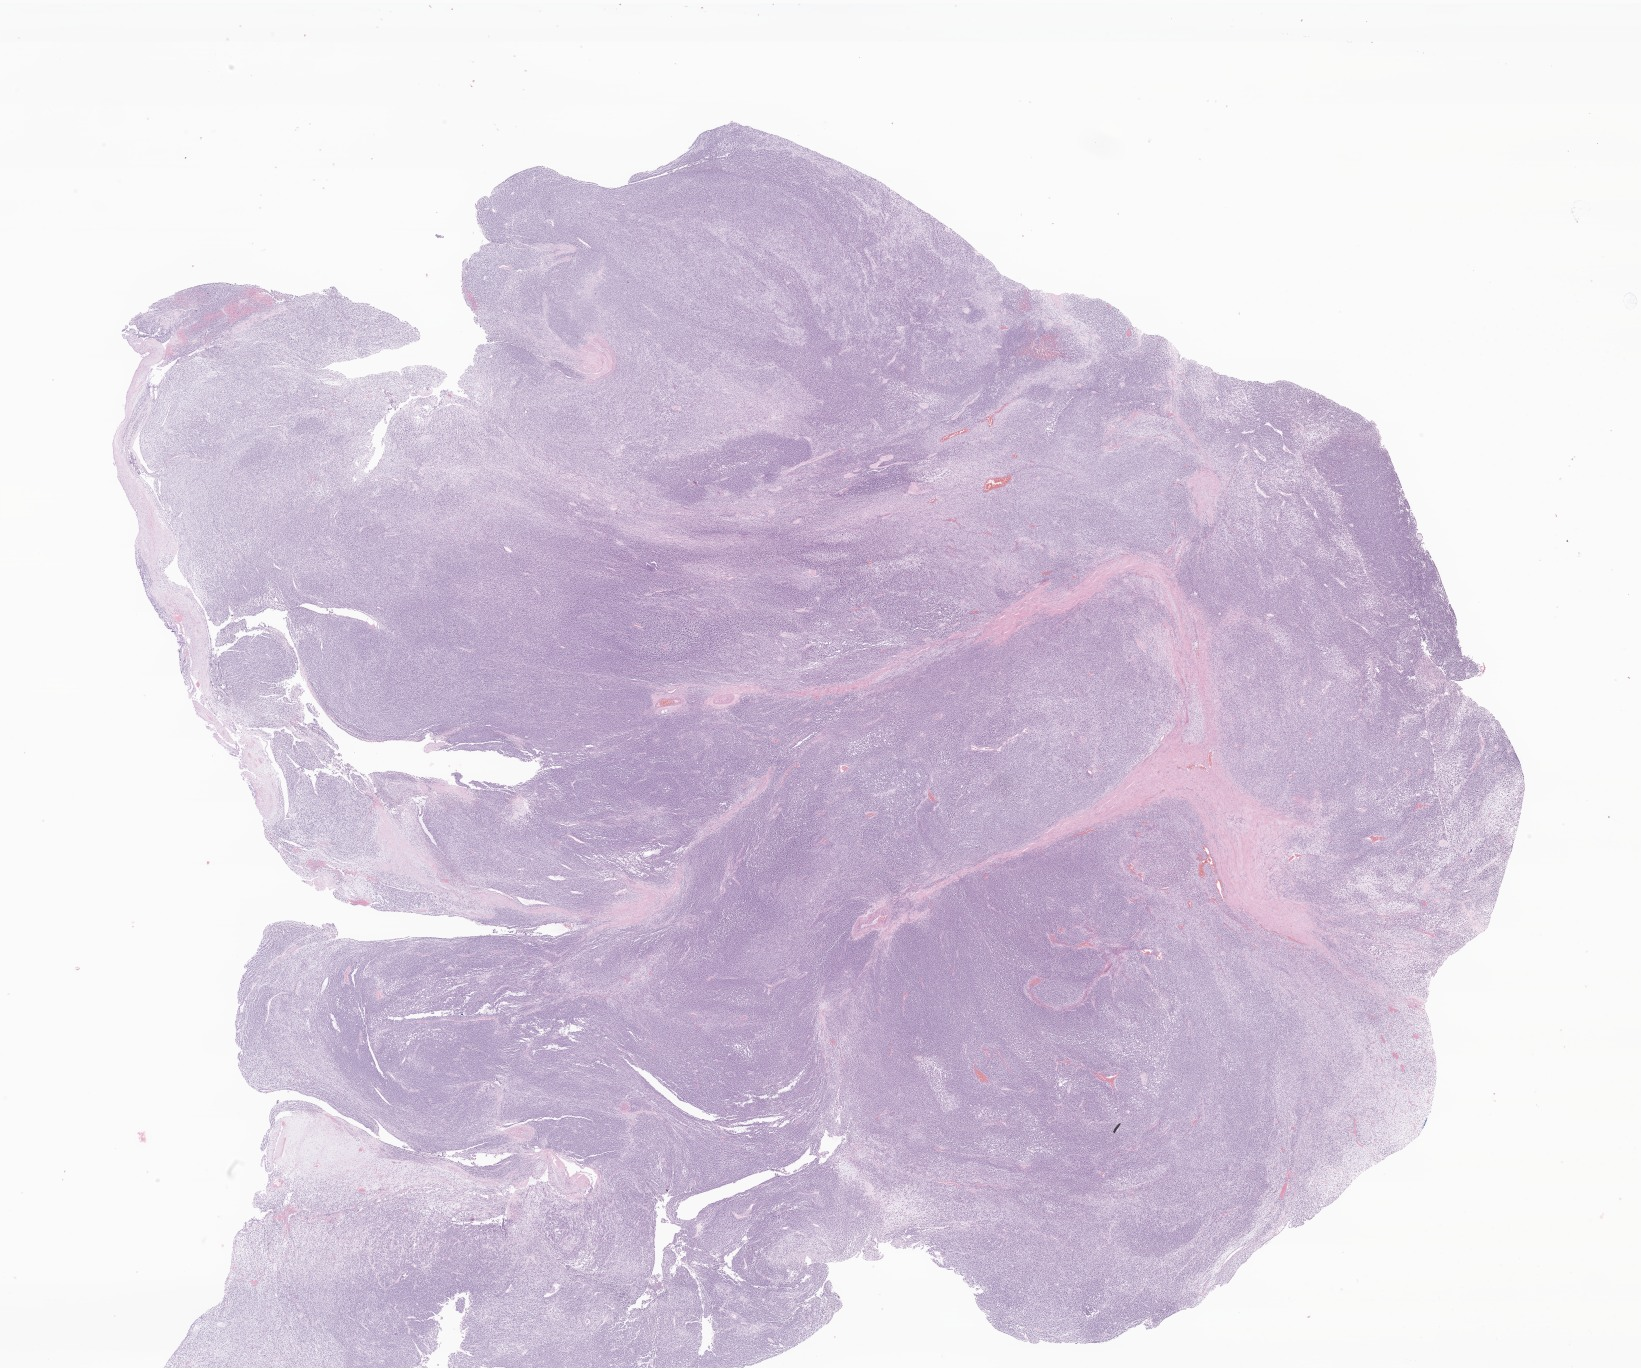
Whole-slide image, hematoxylin and eosin (H&E) stain of tumor tissue from the testis, low-resolution overview of the scanned area, about 27.7 x 23.1 mm. Formalin-fixed, paraffin-embedded (FFPE) tissue. Male patient, age 256 months (21 years 4 months).
• diagnosis: Embryonal rhabdomyosarcoma, NOS